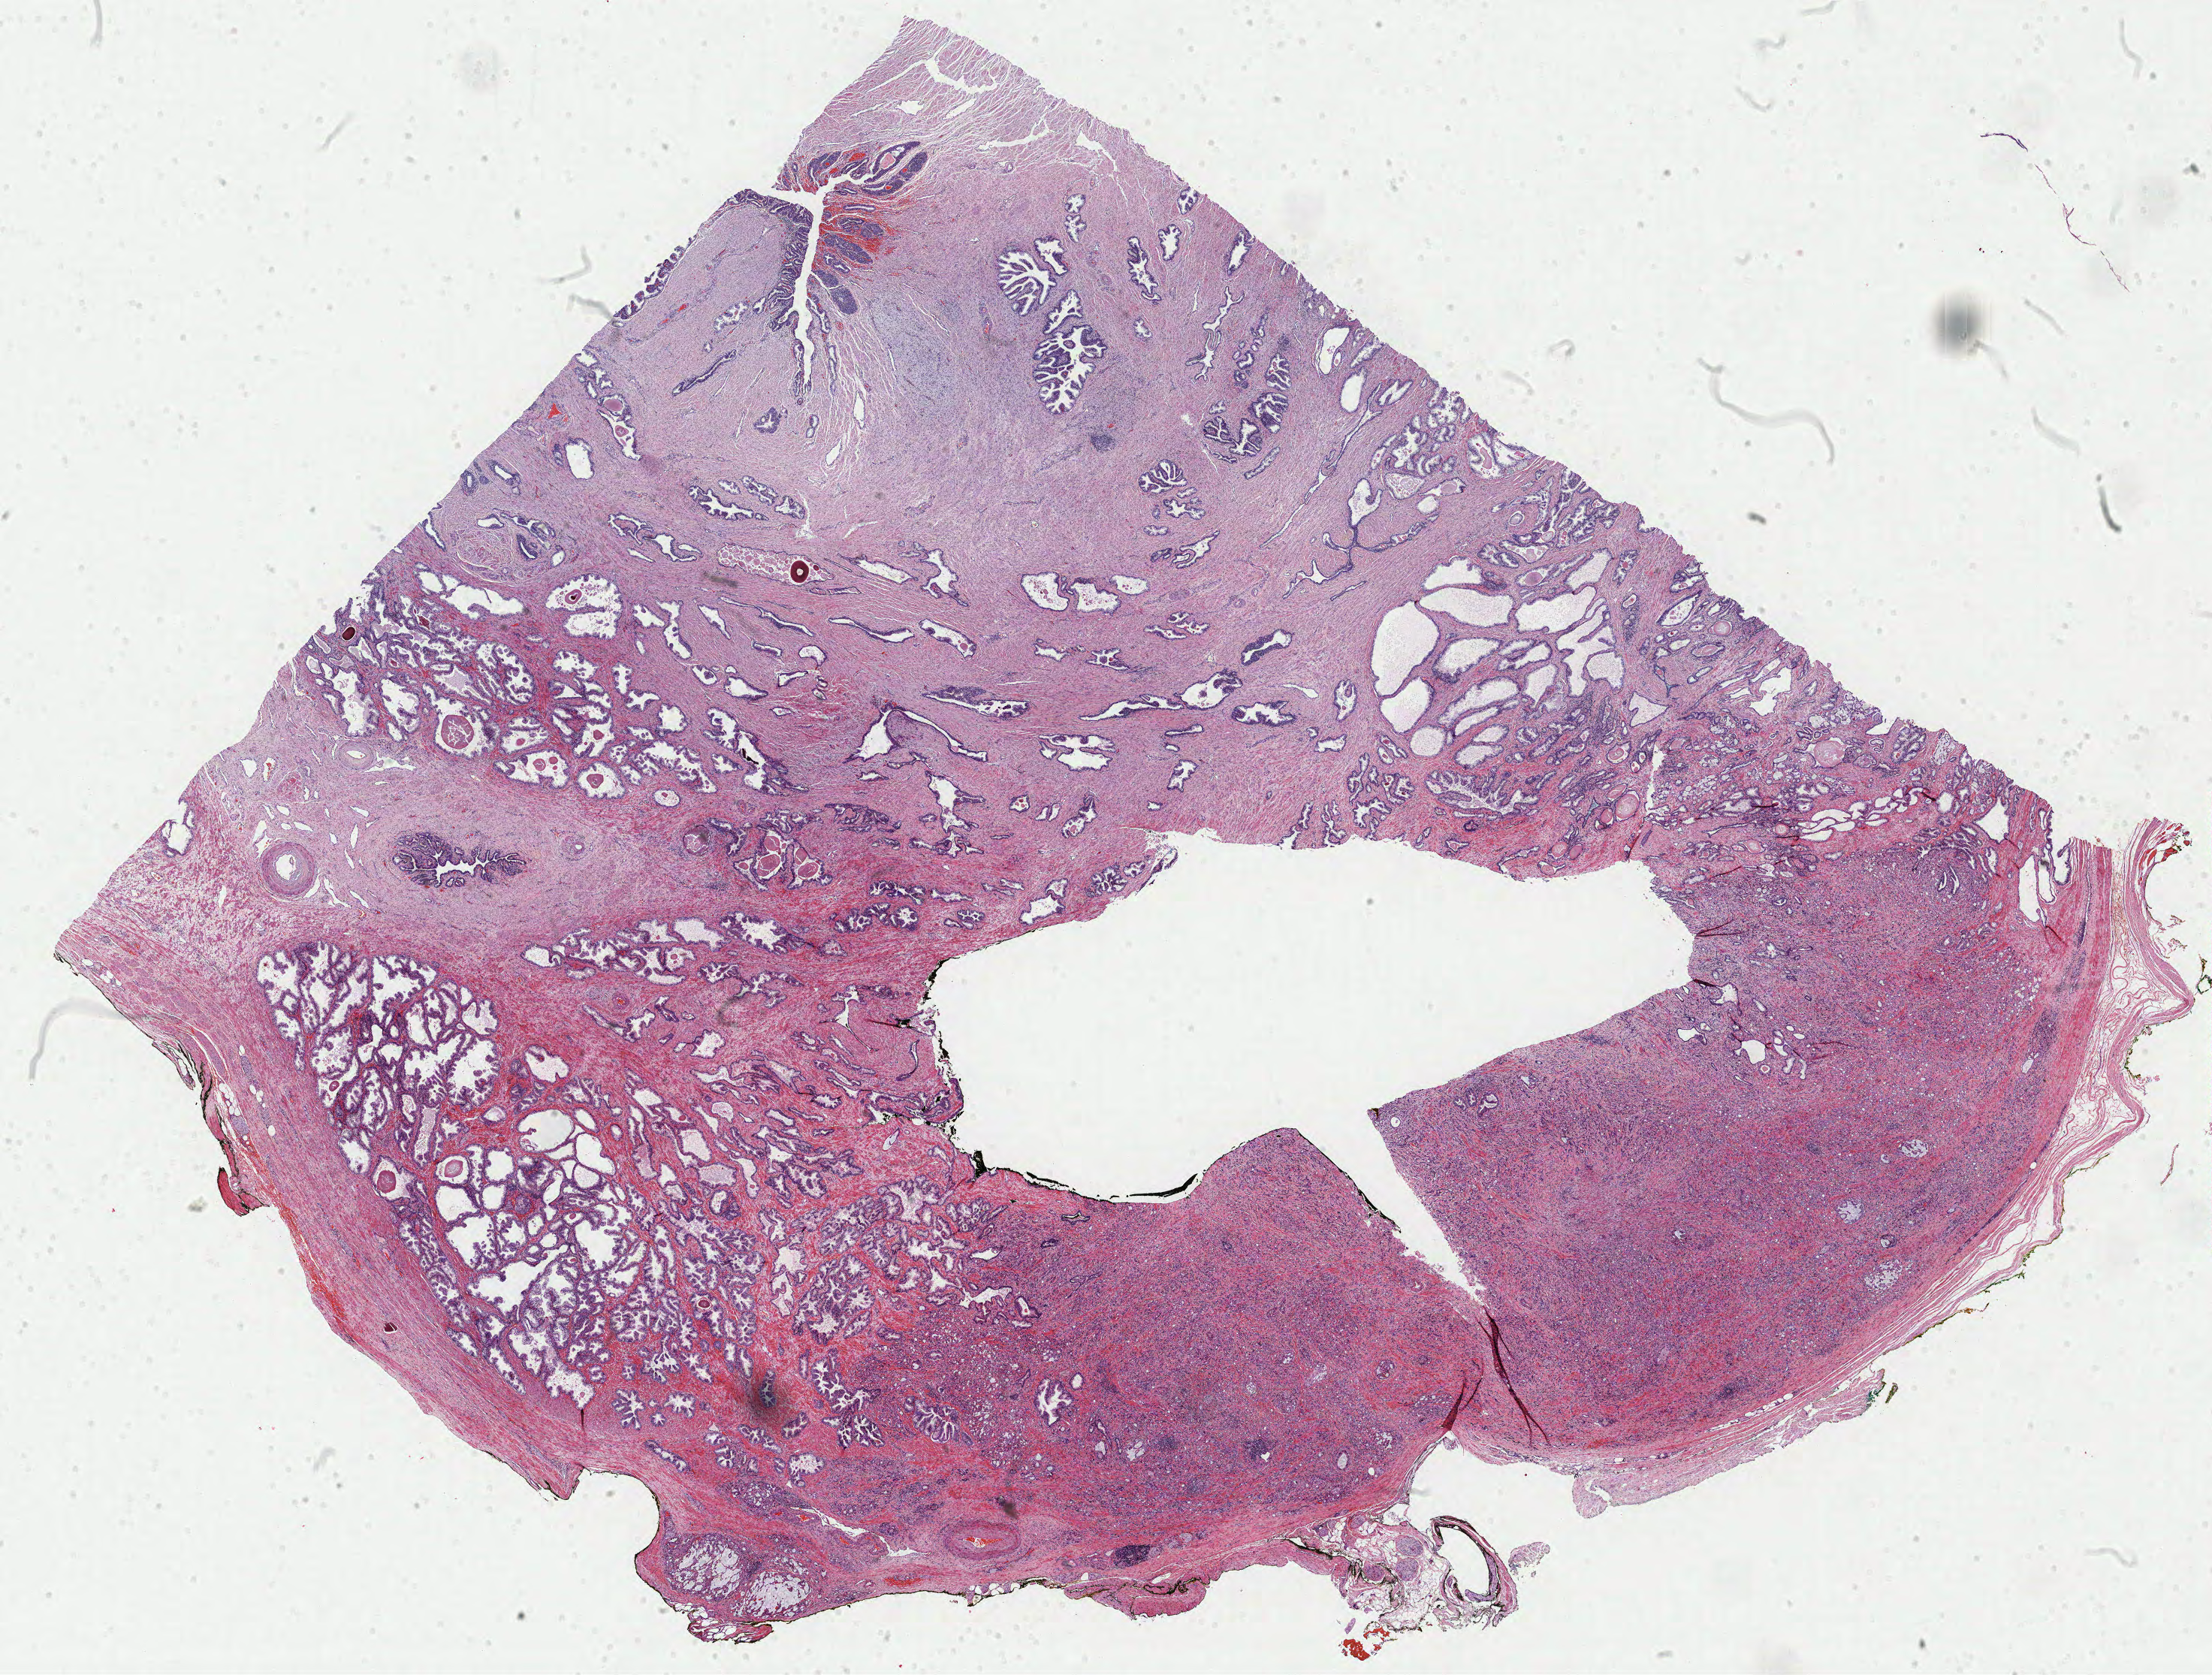
Digitized H&E-stained tissue section (whole slide) — low-resolution overview of the scanned area, about 23.4 x 17.7 mm. FFPE section. Primary tumour sample from the prostate. Patient: male, age at initial diagnosis 68 years. Gleason score: 9 (4+5).
• laterality: left
• pathologic diagnosis: Adenocarcinoma, NOS (prostate gland)